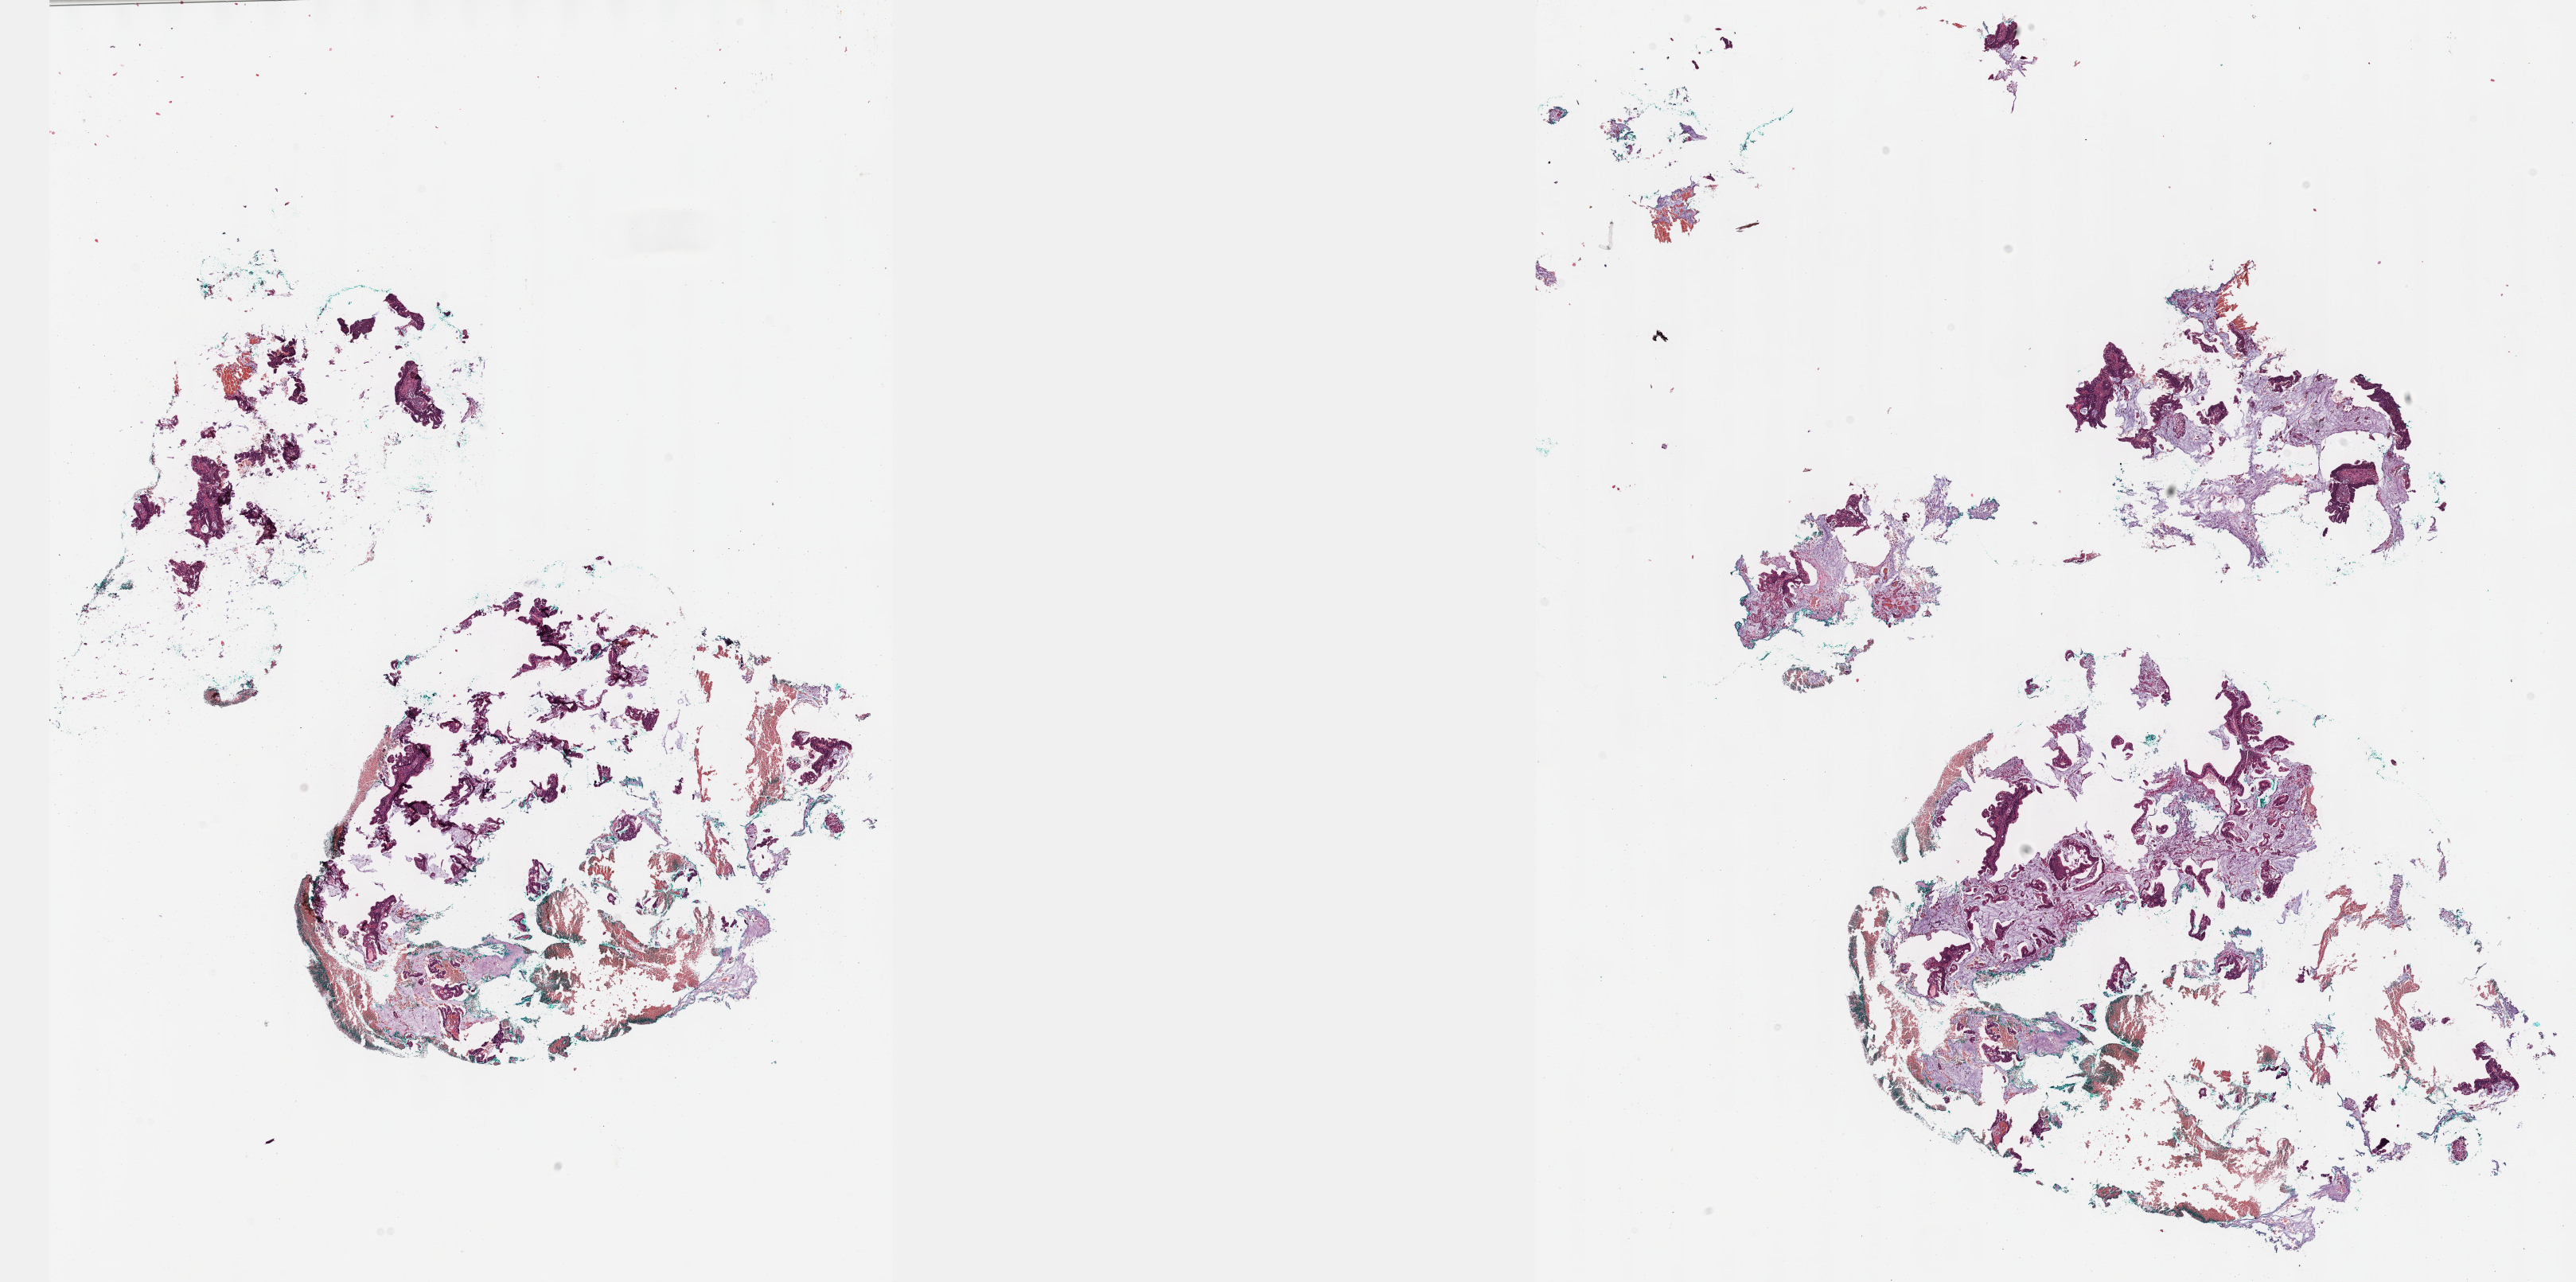
Hematoxylin and eosin (H&E) stained whole-slide image — shown as a low-resolution overview of the whole scanned area (about 26.2 x 13.0 mm); FFPE section; cervix, primary tumour sample. Patient: female, age at initial diagnosis 76 years.
Histologic diagnosis: Mucinous adenocarcinoma, endocervical type (cervix uteri).